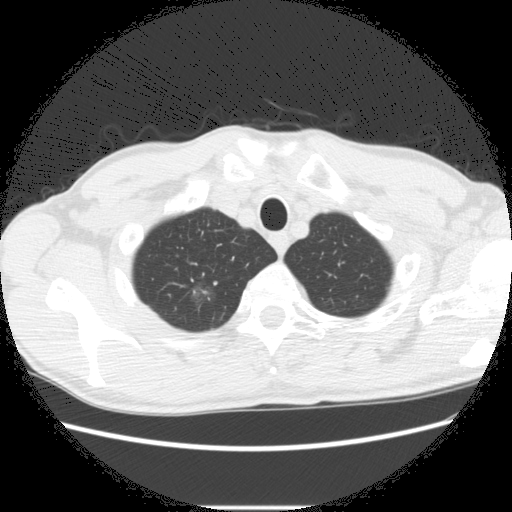
Axial slice from a low-dose chest CT screening exam. Second screening round (one year after baseline). Lung window (W 1500 / L -600 HU). Standard (soft-tissue) reconstruction kernel (STANDARD). 120 kVp. Slice 30 of 282 in the series. 512 × 512 image matrix, field of view 360 × 360 mm. Male participant, aged 66 years at enrolment. Former smoker at enrolment.
Expert reader's lesion annotation, bounding box <173,280,230,325> (left, top, right, bottom; pixels). The screening reader recorded 5 non-calcified nodules or masses ≥4 mm on this exam; which of them this box marks is not recorded. Official screen result: positive, change unspecified: nodule(s) >= 4 mm or enlarging nodule(s), mass(es), or other non-specific abnormalities suspicious for lung cancer. Lung cancer was diagnosed 75 days after this screen: adenocarcinoma, NOS, right upper lobe, undifferentiated (G4), stage IA (AJCC 6th edition), 20 mm at pathology.